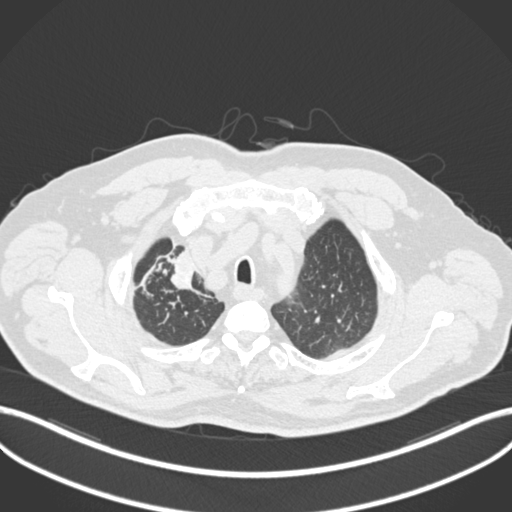
Chest CT, one axial slice. Slice 173 of 255 in the series (ordered by position). Reconstruction kernel B30f. 120 kVp. Lung window (W 1500 / L -600 HU). 512 × 512 image matrix, field of view 400 × 400 mm. Patient: male, 60 years. Case-level facts recorded for this patient, not image findings: clinical TNM (as recorded): T1b N1 M0.
Outlined on this slice (bounding box drawn by a radiologist):
- lung tumour (recorded histology: squamous cell carcinoma): bounding box (x1, y1, x2, y2) in pixels: (165, 248, 204, 296)